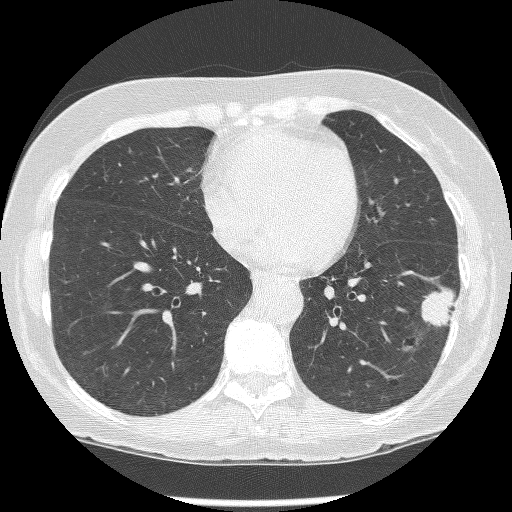
Axial slice from a low-dose chest CT screening exam, baseline annual screen, lung window (W 1500 / L -600 HU), 1.25 mm slice thickness, slice 95 of 247 in the series. Female, age 62 years at enrolment. Former smoker at enrolment.
• Lesion marked by an expert reader, bounding box (x1, y1, x2, y2) in pixels: (417, 283, 461, 338).
• The screening reader recorded 2 non-calcified nodules or masses ≥4 mm on this exam (left lower lobe, left lower lobe); which of them this box marks is not recorded.
• Participant outcome: lung cancer diagnosed 15 days after this screen — non-small cell carcinoma, left lower lobe, stage IIIB (AJCC 6th edition), 23 mm at pathology.